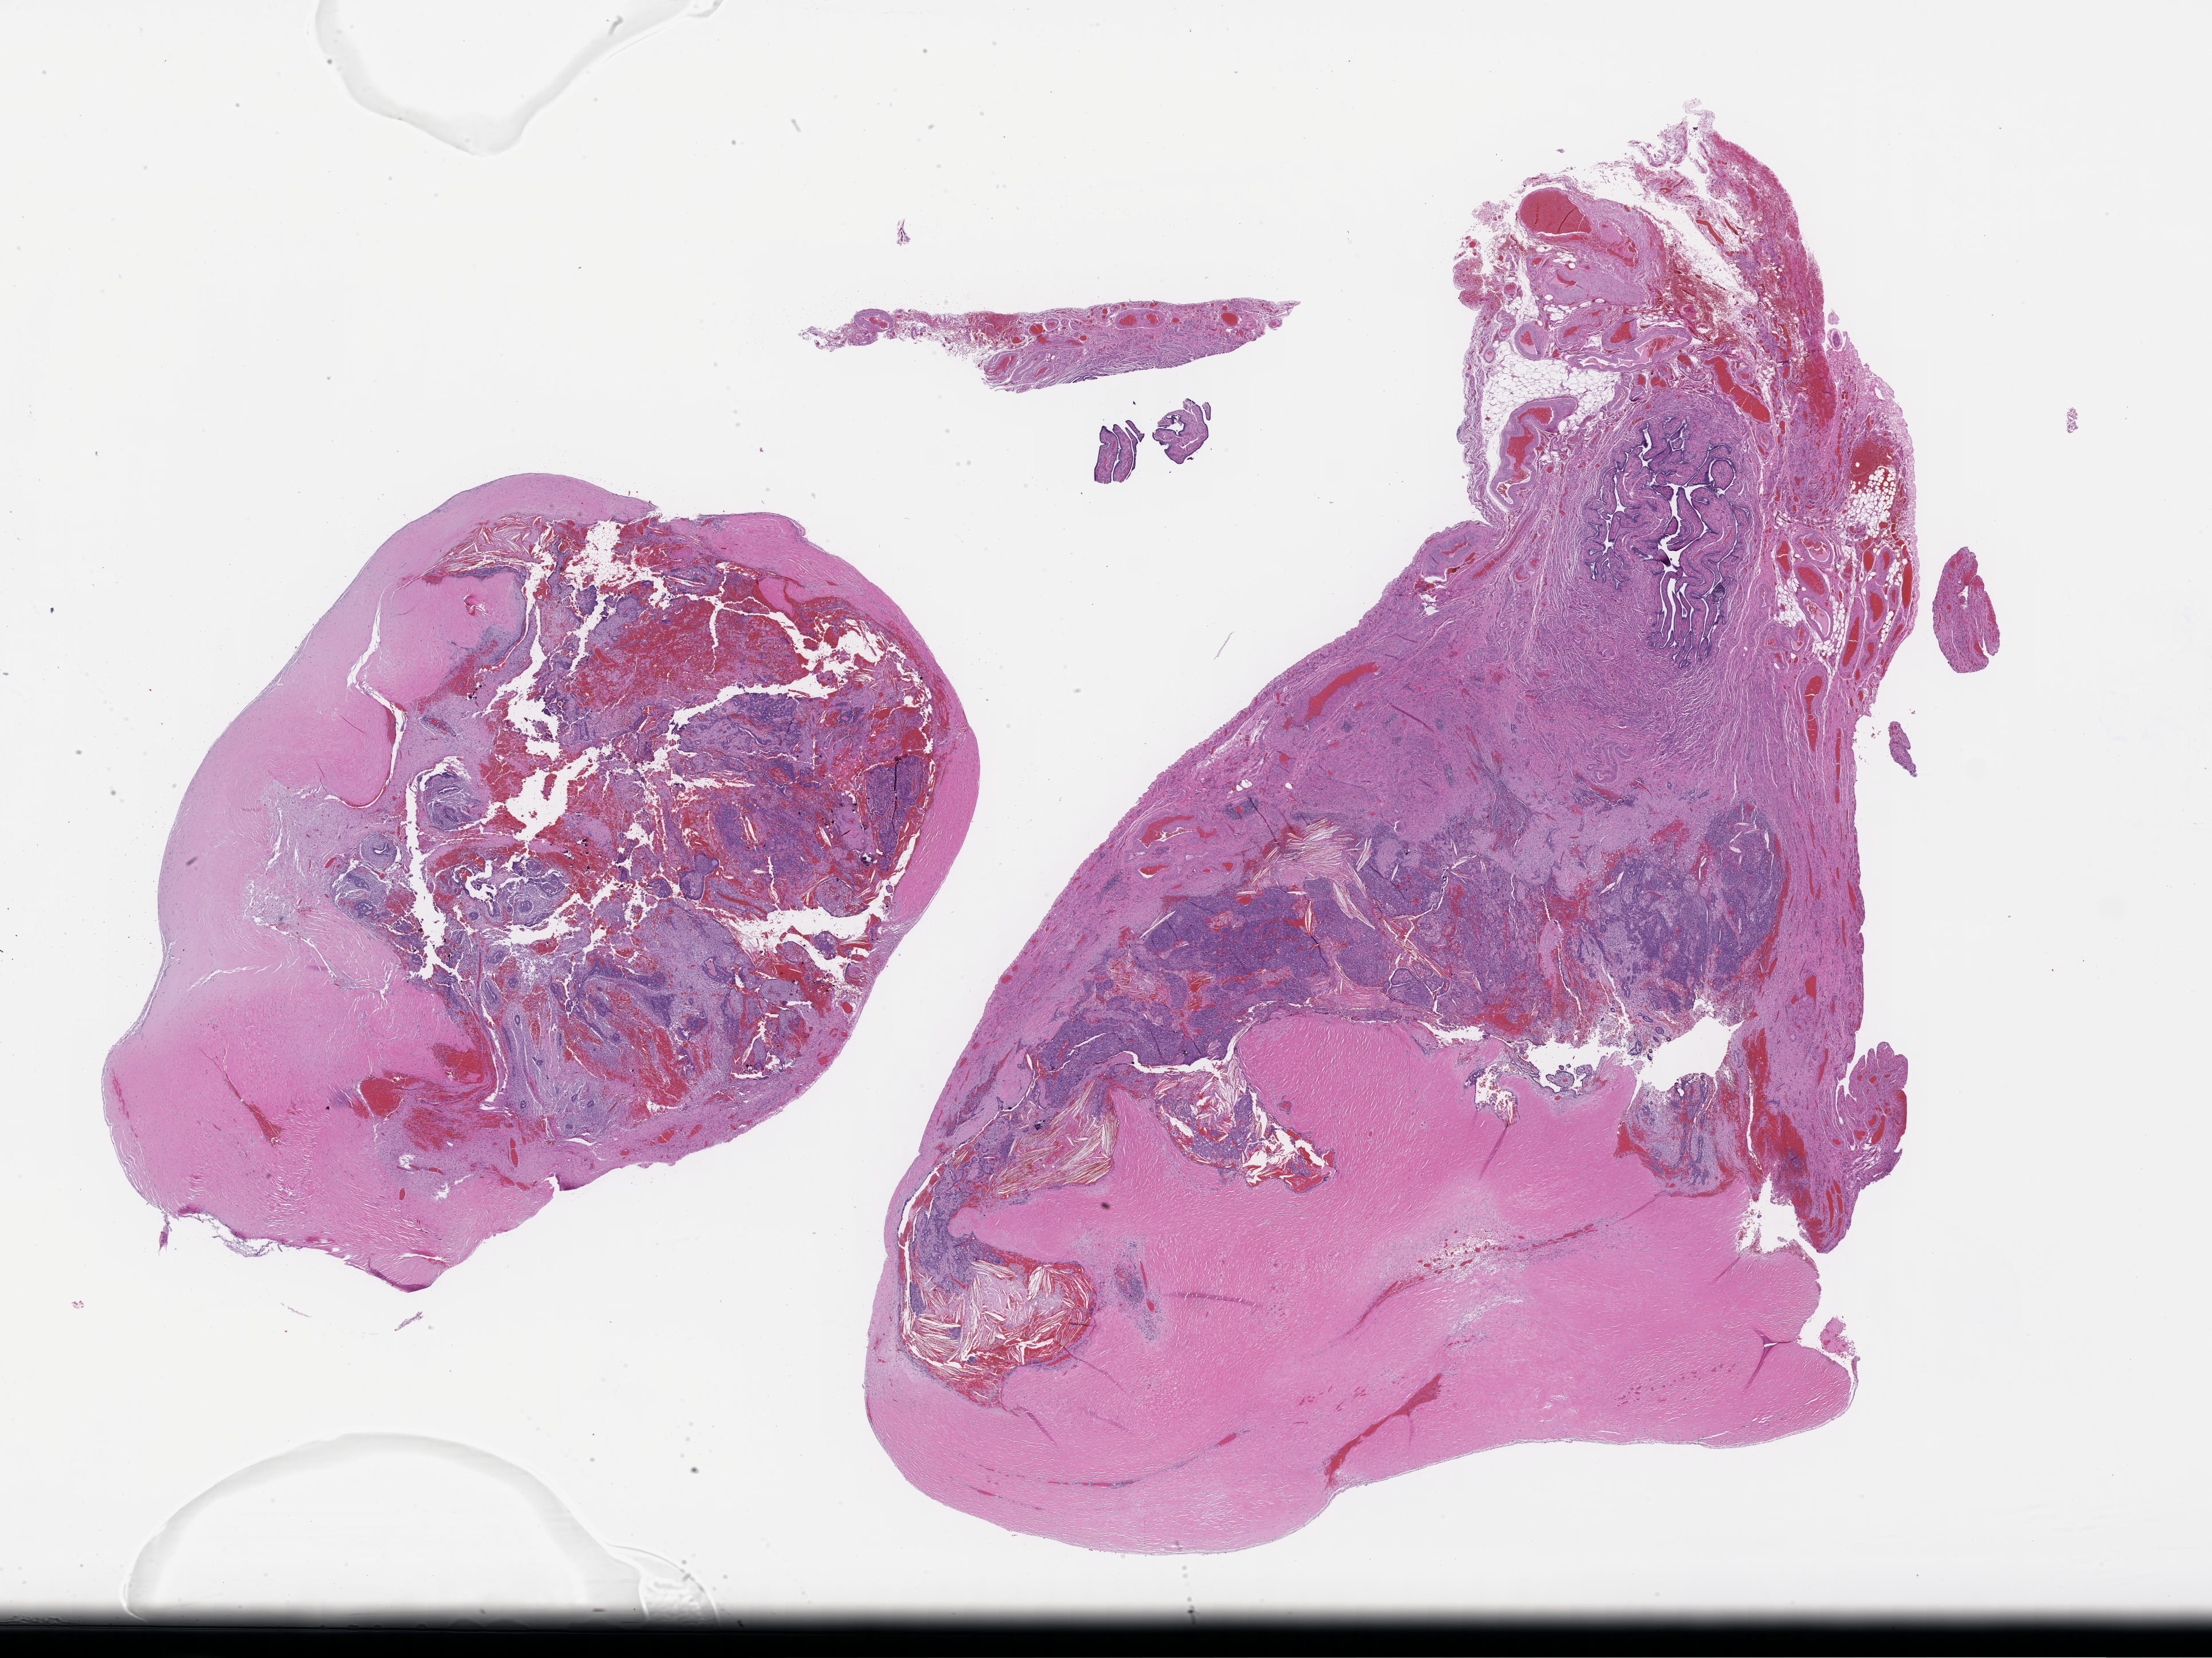
Haematoxylin and eosin whole-slide image — a low-resolution overview of the entire scanned area, about 31.2 x 23.4 mm; FFPE section; site: ovary; specimen time point: archival tissue. Patient: female.
This section: primary tumor. Diagnosis: Ovarian Carcinoma.